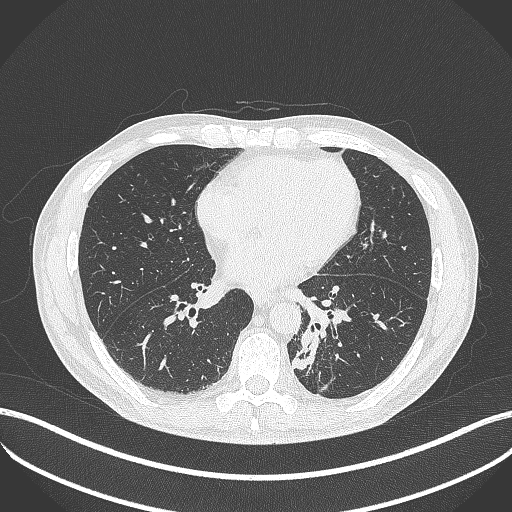
Chest CT, one axial slice; position 165 of 451 along the scan axis; 120 kVp; lung window (W 1500 / L -600 HU); 512 × 512 image matrix, field of view 400 × 400 mm. Patient: male, 72 years. From the clinical record (not read from this slice): clinical TNM (as recorded): T2b N0 M1.
Outlined on this slice (rectangle marked by the reading radiologist):
- lung tumour (recorded histology: adenocarcinoma): bounding box (x1, y1, x2, y2) in pixels: (288, 321, 320, 375)